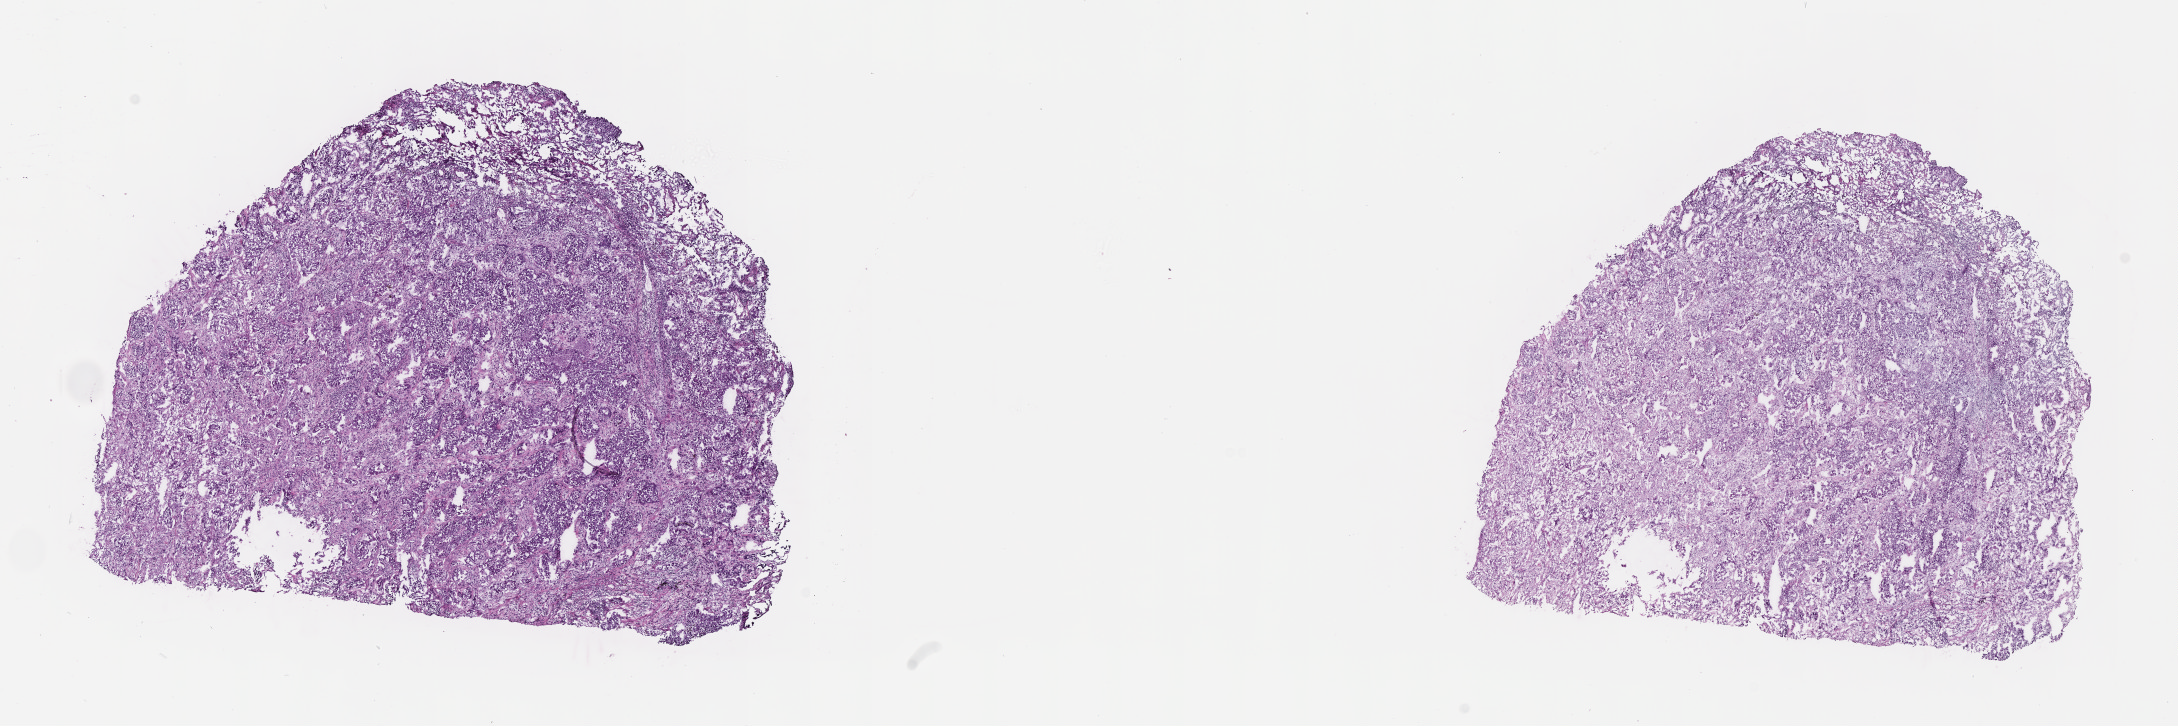
Digitized haematoxylin and eosin-stained section, whole scanned area (about 17.6 x 5.9 mm) shown as a low-resolution overview. Frozen section (tissue freezing medium). Specimen: primary tumor. Site: lower lobe of right lung. Patient: male, age 52 years. Pathologist review of this section (percent, as recorded): tumor cells 85%, tumor nuclei 65%, stromal cells 0%, necrosis 5%, normal cells 10%. Infiltration values recorded for this section: lymphocyte infiltration 0%, monocyte infiltration 0%, neutrophil infiltration 0%.
• diagnosis: Adenocarcinoma, NOS
• AJCC pathologic stage: Stage IIIA
• section: top of the tissue portion